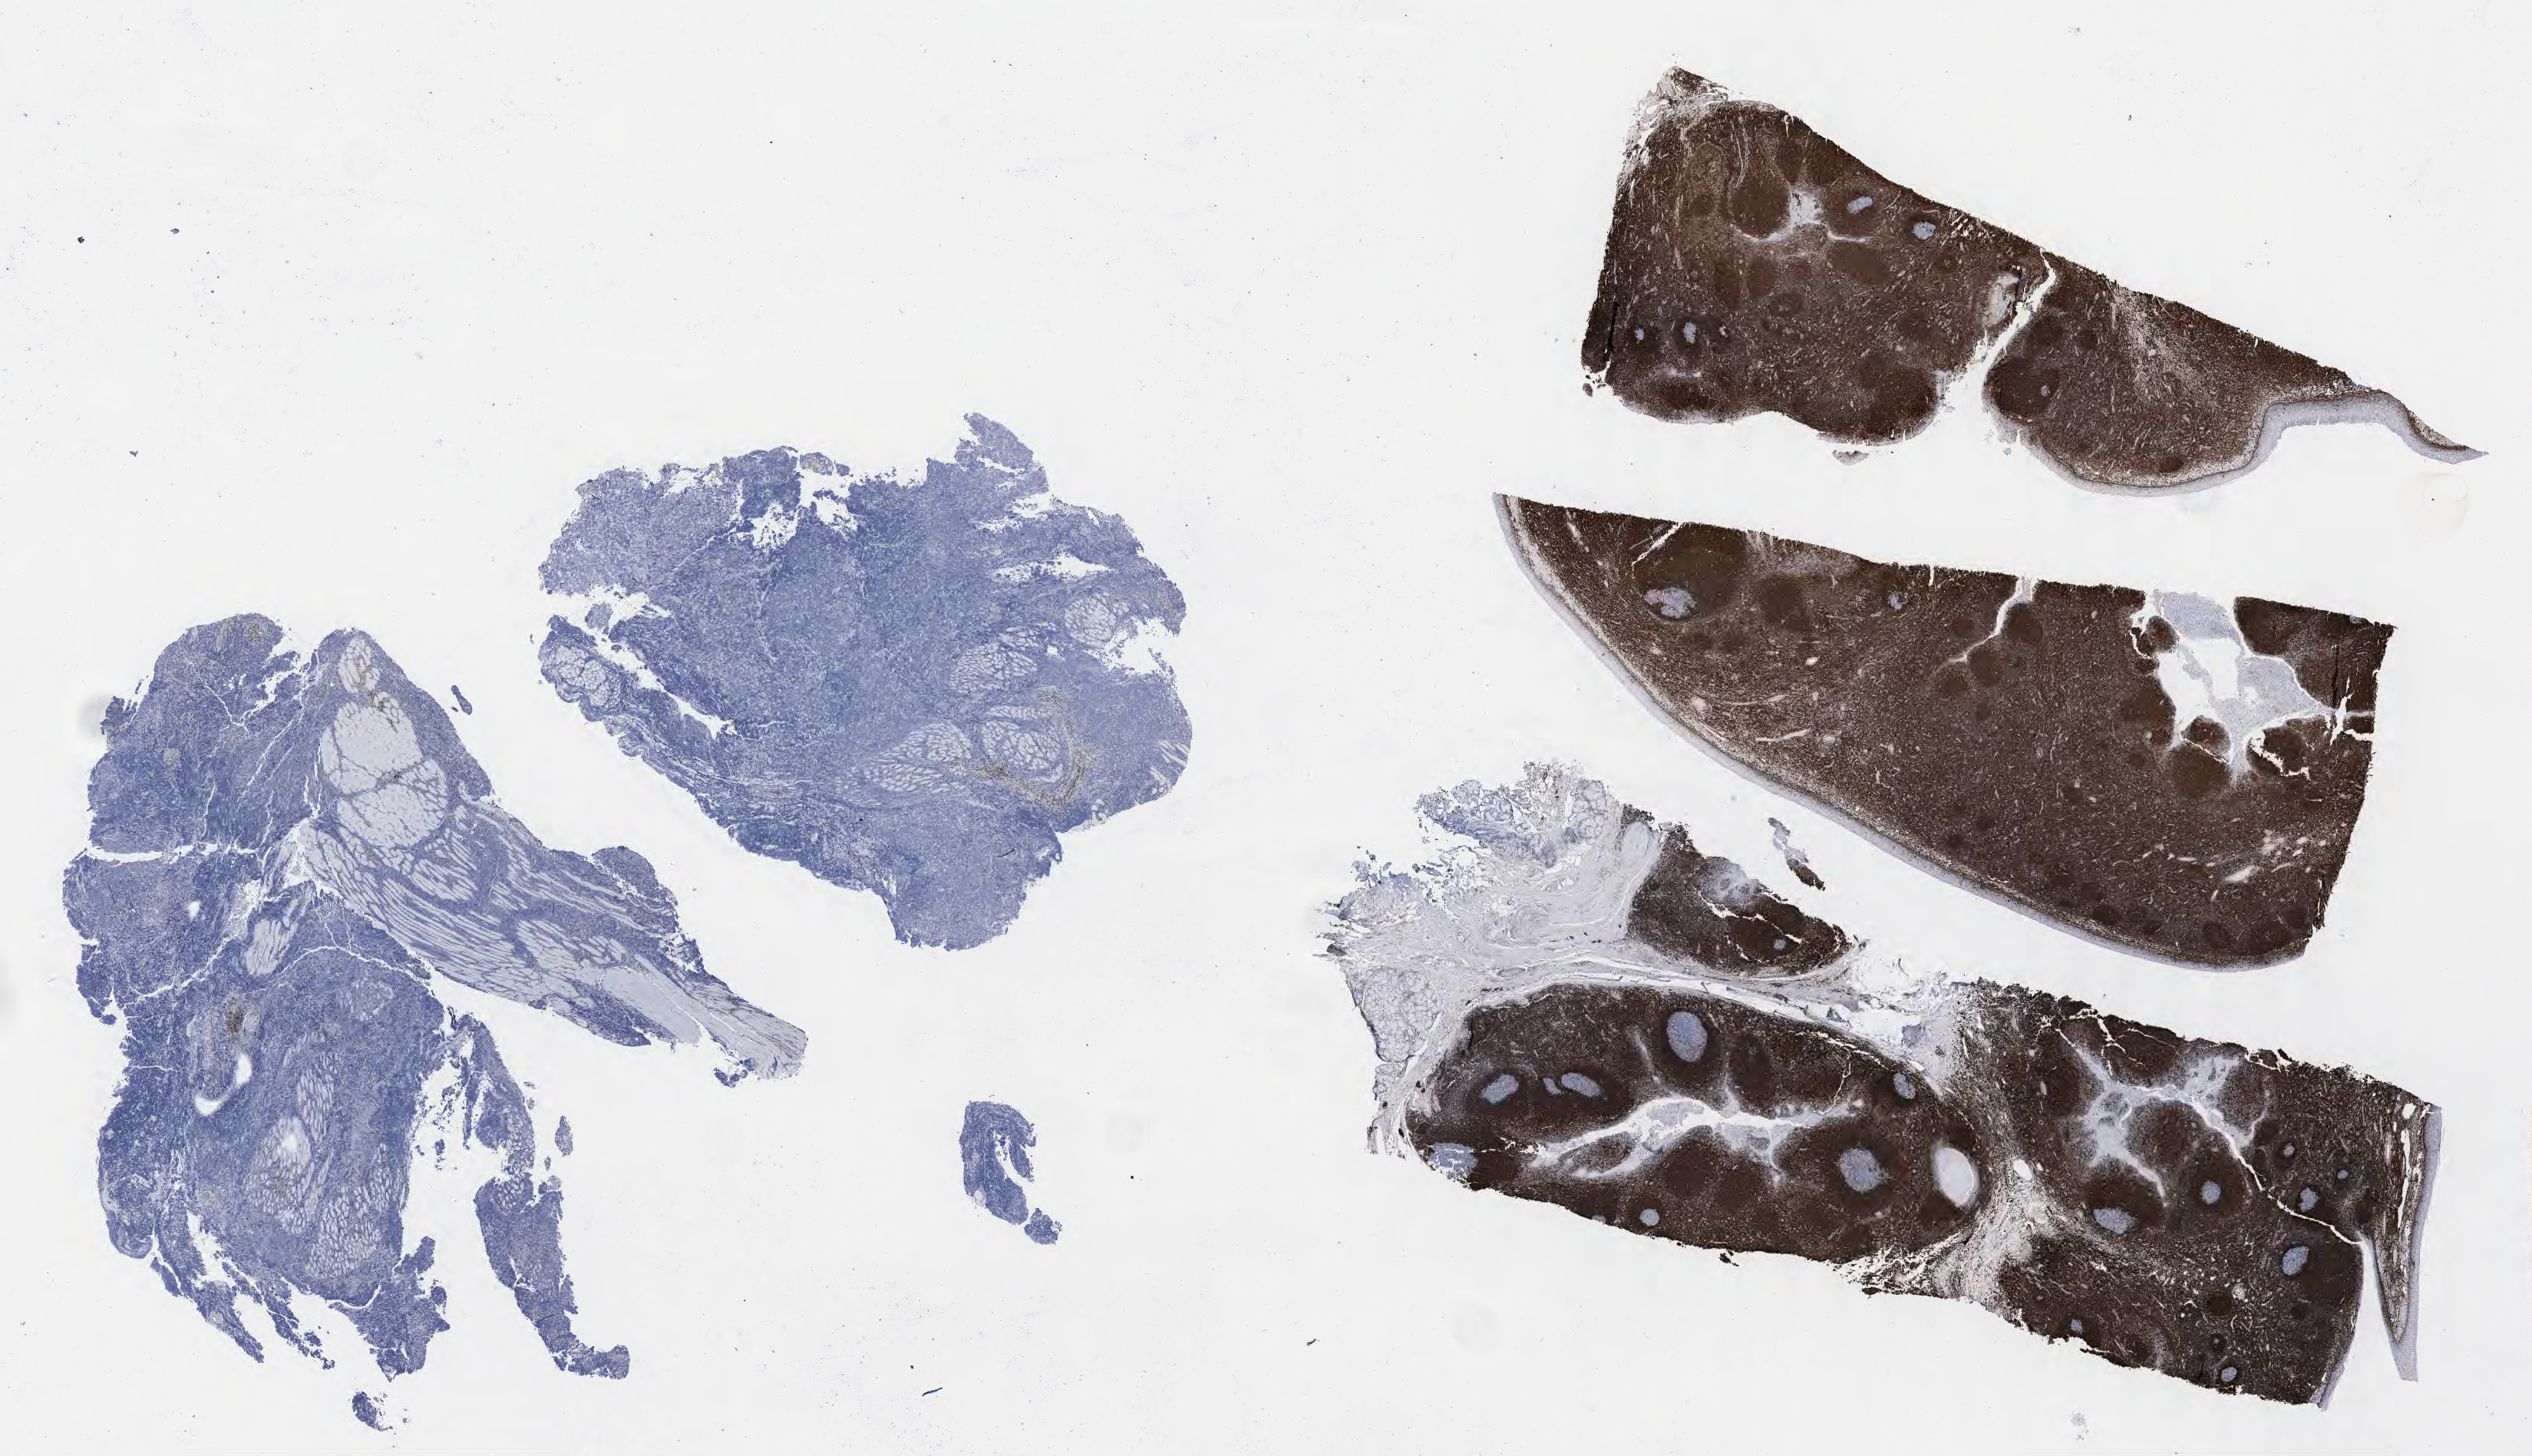
IHC for BCL2, whole-slide image — whole scanned area (about 26.7 x 15.3 mm) shown as a low-resolution overview, tumor tissue, site: pelvis. Male, age 7 years at initial diagnosis.
Diagnosis: Diffuse large B-cell lymphoma, NOS.